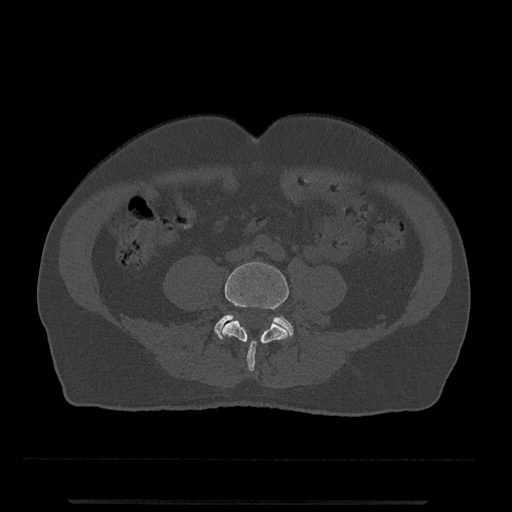
CT including the spine, one axial slice. Position 115 of 797 along the scan axis. 120 kVp. Bone window (W 1800 / L 400 HU). 0.5 mm slice thickness. 512 × 512 image matrix, field of view 419 × 419 mm. Male patient, age 63 years. Case-level facts recorded for this patient, not image findings: primary cancer: prostate.
Structures marked on this image (semi-automatically segmented with operator editing):
- L4 vertebra: box from (x=222, y=262) to (x=289, y=372) px
- L5 vertebra: (x=215, y=314)–(x=293, y=339)